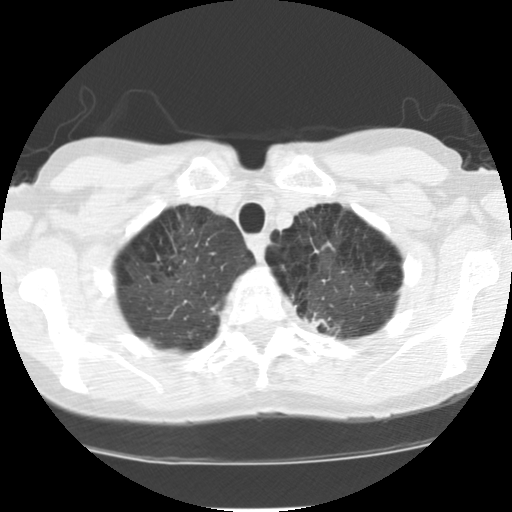
Low-dose screening chest CT, one axial slice. Position 101 of 116 along the scan axis. Reconstruction kernel STANDARD. 120 kVp. Lung window (W 1500 / L -600 HU). 2.5 mm slice thickness. 512 × 512 image matrix.
Annotated regions visible in this slice (outlined manually by an expert reader):
- lesion 1 (tumor, upper lobe of left lung): box from (x=306, y=313) to (x=334, y=331) px